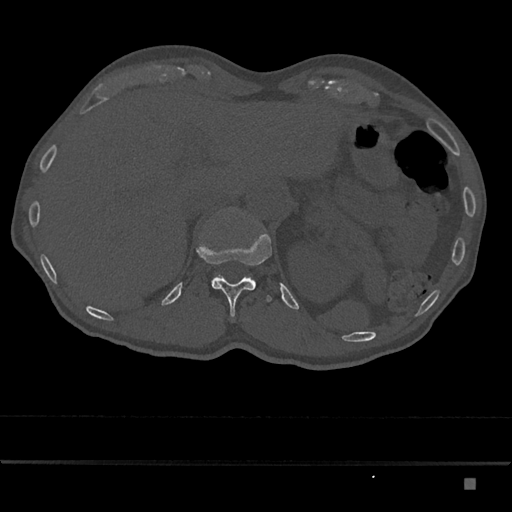
CT including the spine, one axial slice. Slice 602 of 797 in the series (ordered by position). Reconstruction kernel Br40s/3. 120 kVp. Bone window (W 1800 / L 400 HU). 512 × 512 image matrix, field of view 390 × 390 mm. Male patient, age 72 years. From the clinical record (not read from this slice): primary cancer: prostate.
Outlined on this slice (semi-automatically segmented with operator editing):
- T12 vertebra: bounding box (x1, y1, x2, y2) in pixels: (197, 233, 272, 317)